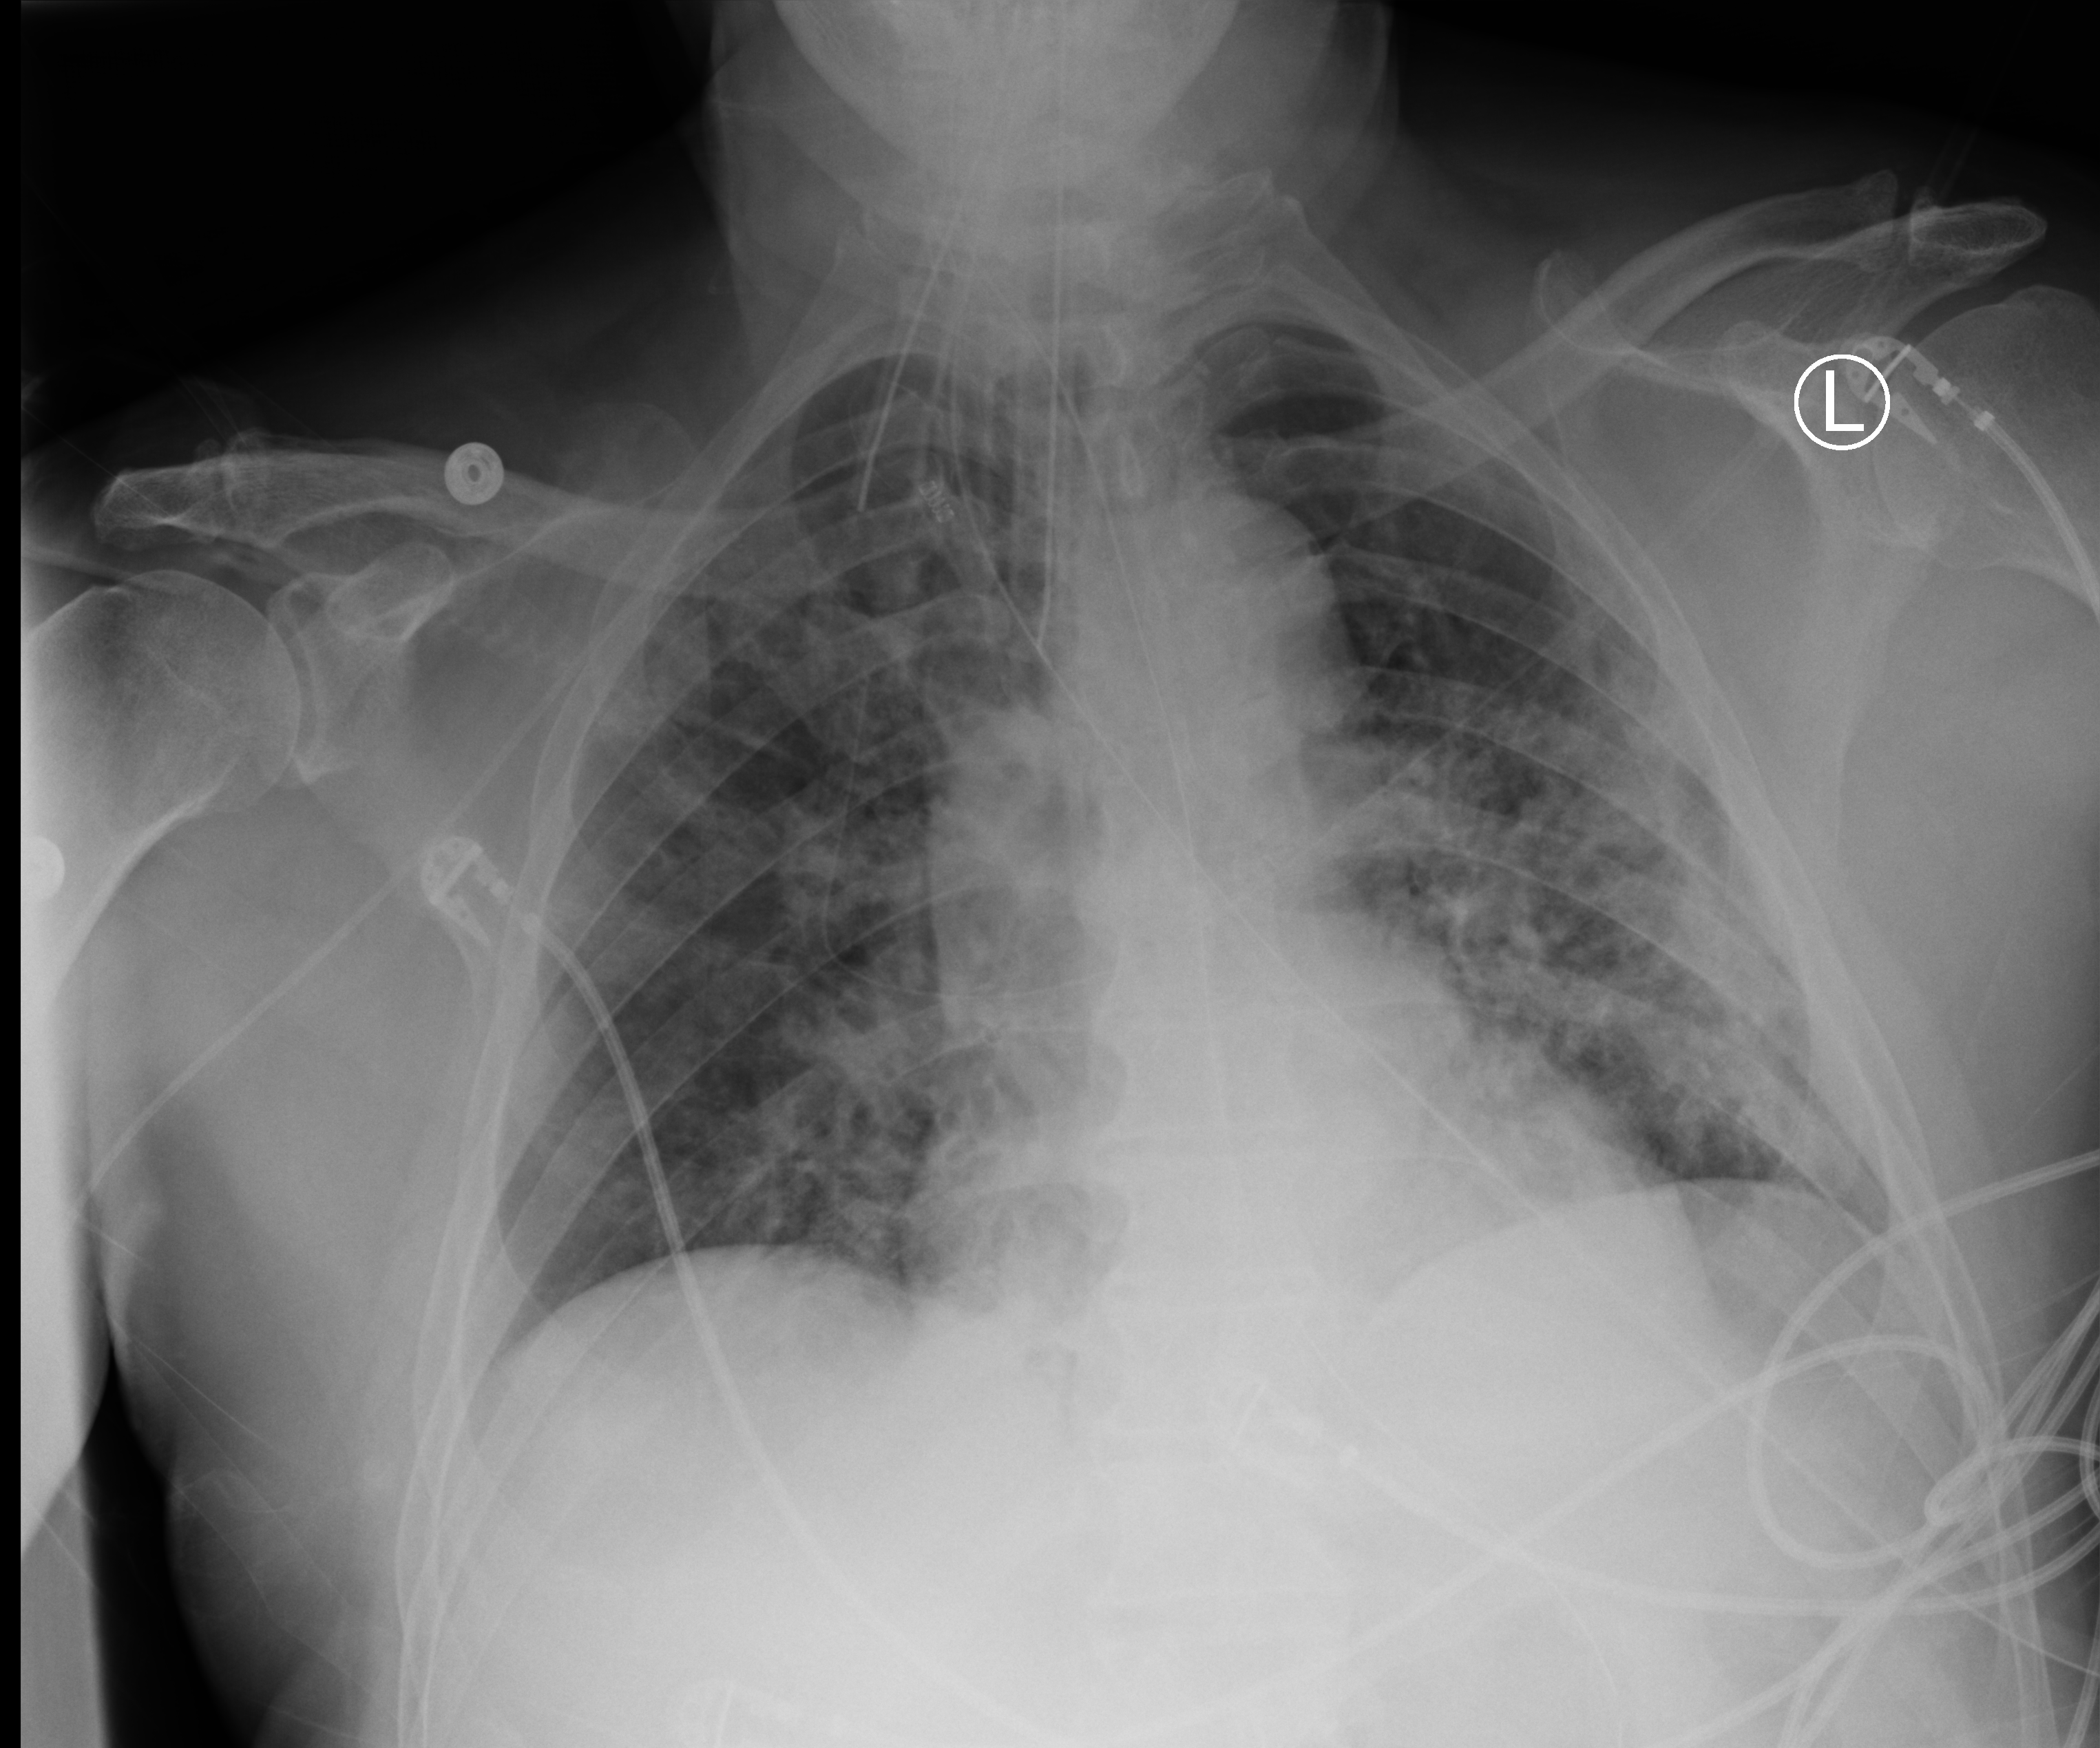
Portable chest radiograph; anteroposterior (AP) projection. Male patient hospitalised with COVID-19, age 60–74 years.
Hospital-stay facts (about this admission, not read from this image; timing relative to this image not recorded): admitted to intensive care during this hospital stay: yes.